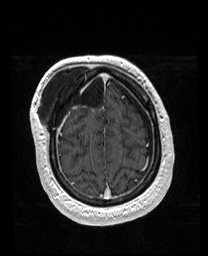
Brain MRI from a brain-tumour surgery series, one axial slice. Position 43 of 176 along the scan axis. T1-weighted post-contrast. 1 mm slice thickness. 208 × 256 image matrix, field of view 208 × 256 mm. Case-level facts recorded for this patient, not image findings: histopathology: Astrocytoma; WHO grade: 4; IDH mutation: yes.
Outlined on this slice (expert manual segmentation):
- previous resection cavity: bounding box <74,74,103,107> (left, top, right, bottom; pixels)